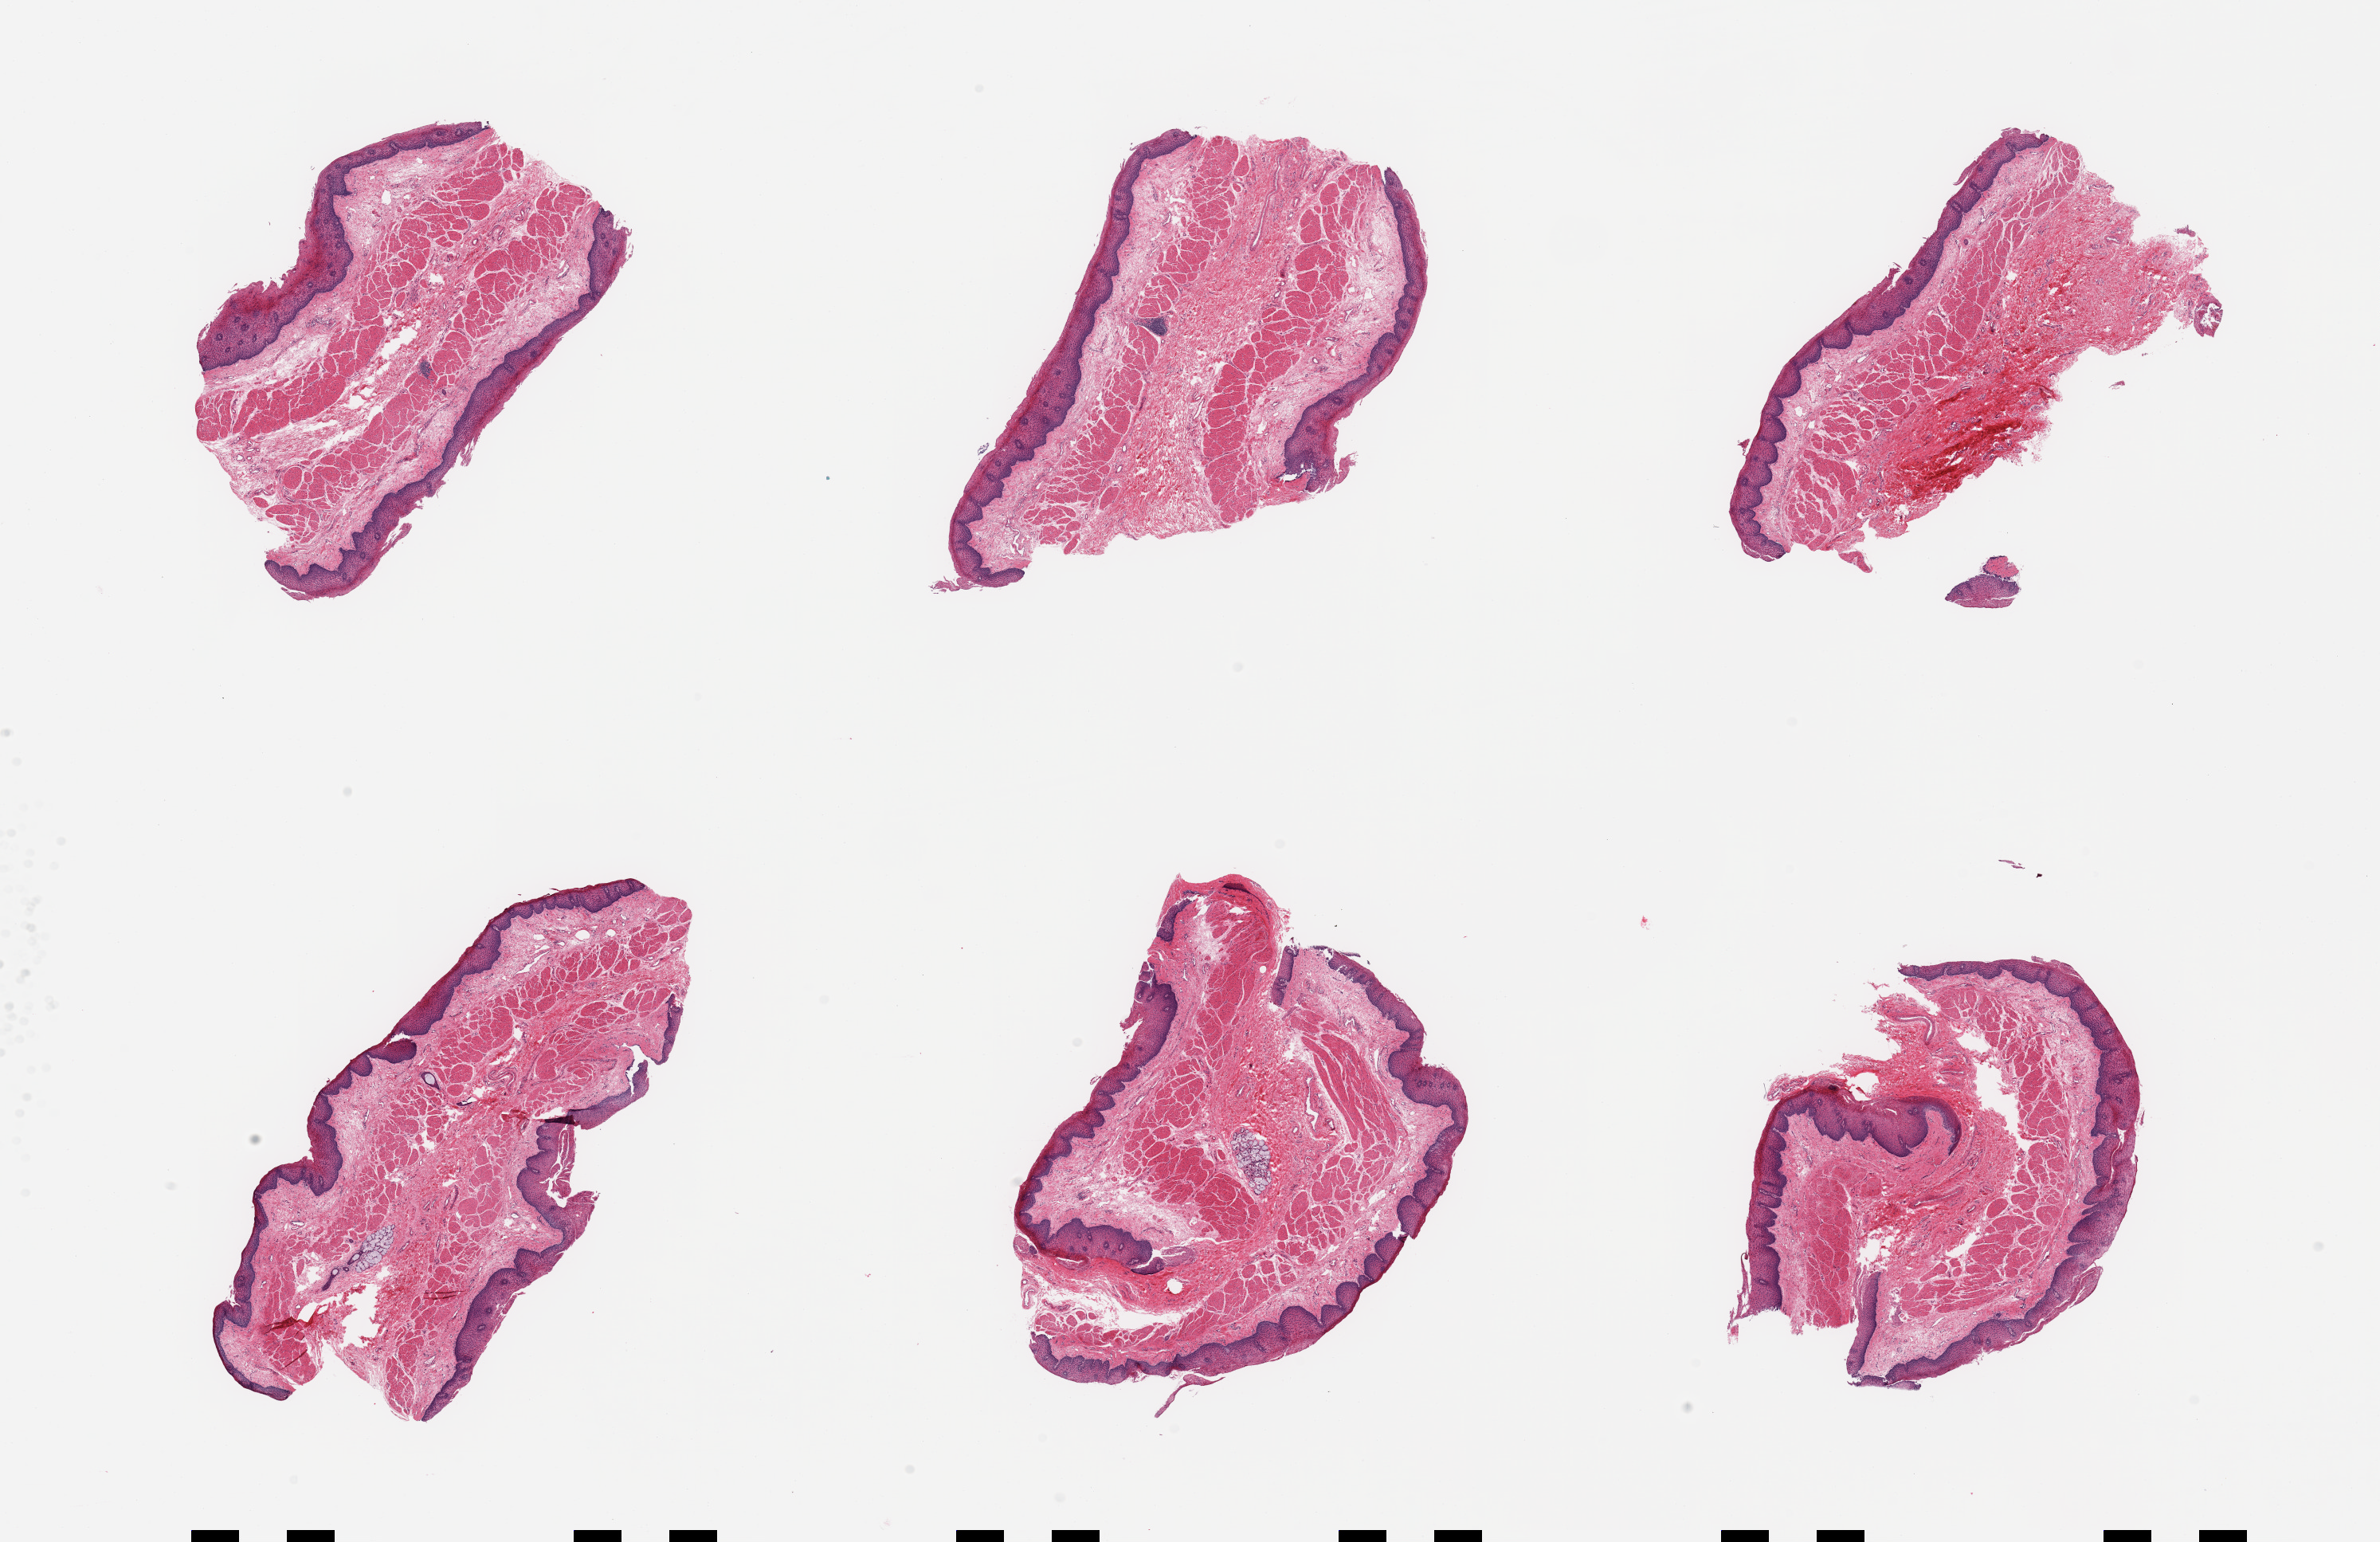
Haematoxylin and eosin whole-slide image — whole scanned area (about 23.6 x 15.3 mm) shown as a low-resolution overview, PAXgene-fixed paraffin-embedded (PFPE) section, target tissue: esophageal mucous membrane, donor tissue sample. Donor sex: male.
Review note (as recorded): 6 pieces.